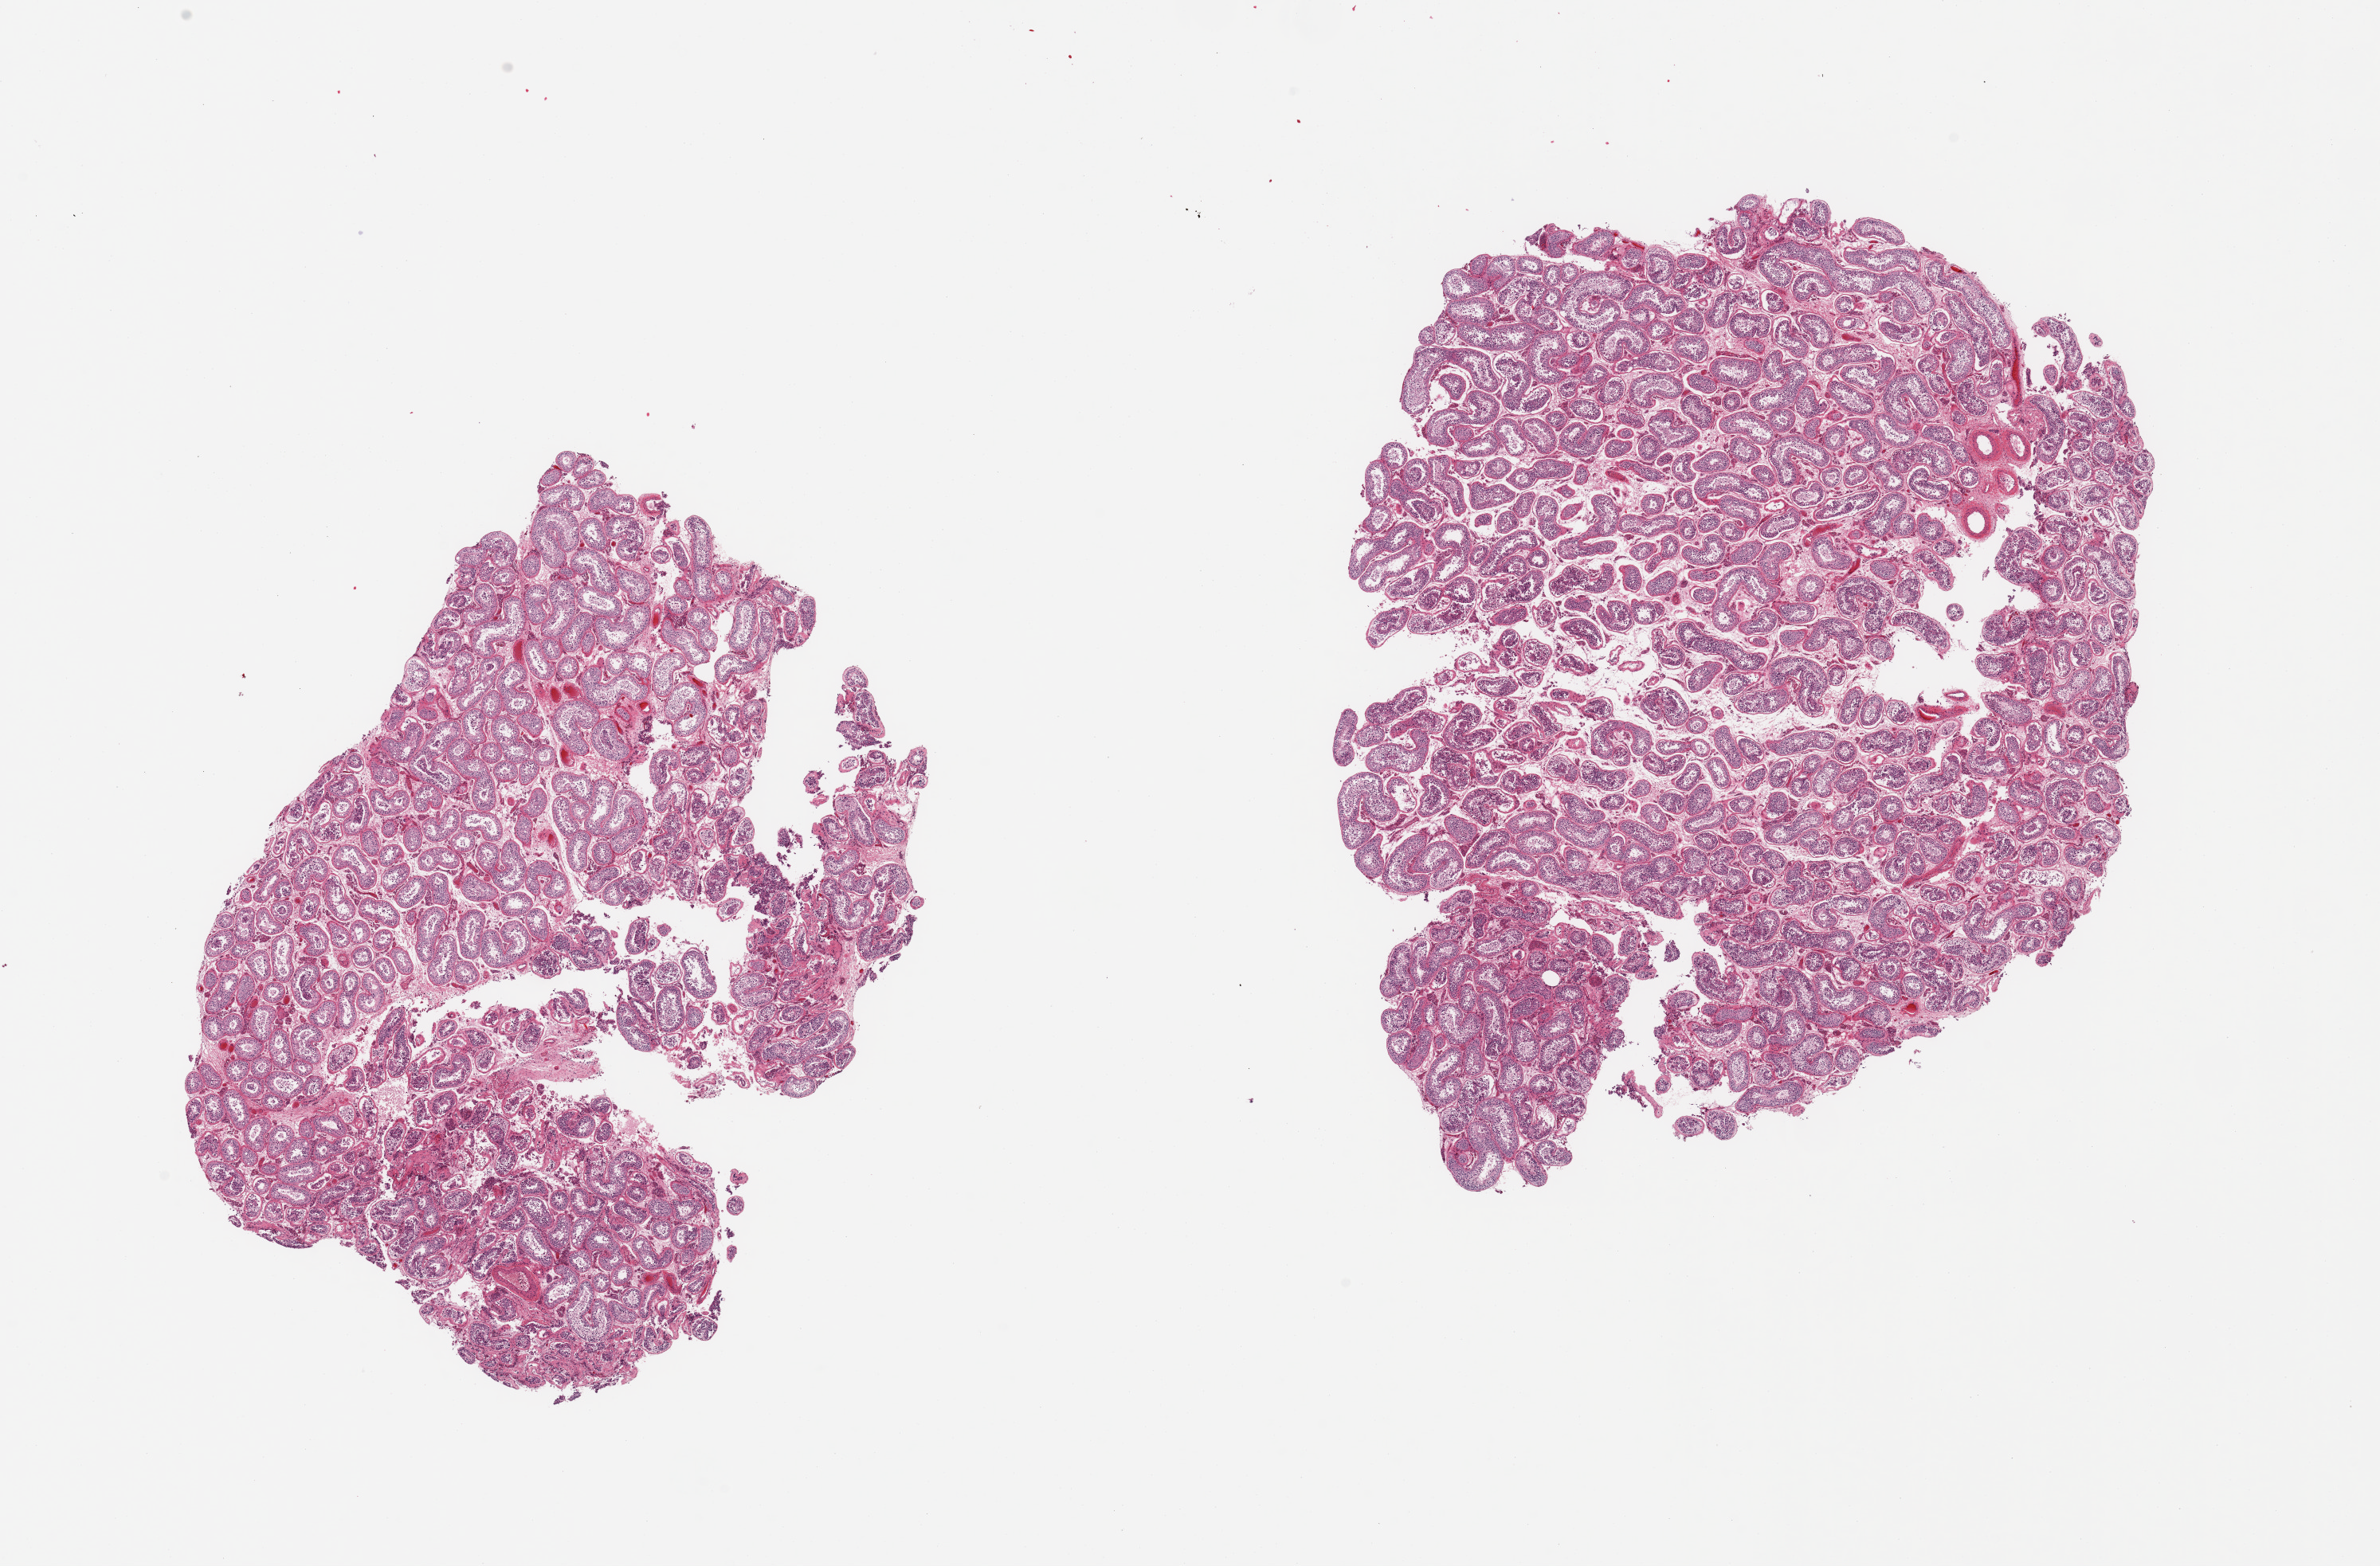
Whole-slide image, H&E stain, brightfield — a low-resolution overview of the entire scanned area, about 23.6 x 15.6 mm. PAXgene-fixed, paraffin-embedded tissue. Section of testis (target tissue). Donor tissue sample. Donor sex: male.
Reviewer comment on this tissue sample: 2 pieces, spermatogenesis appears reduced.